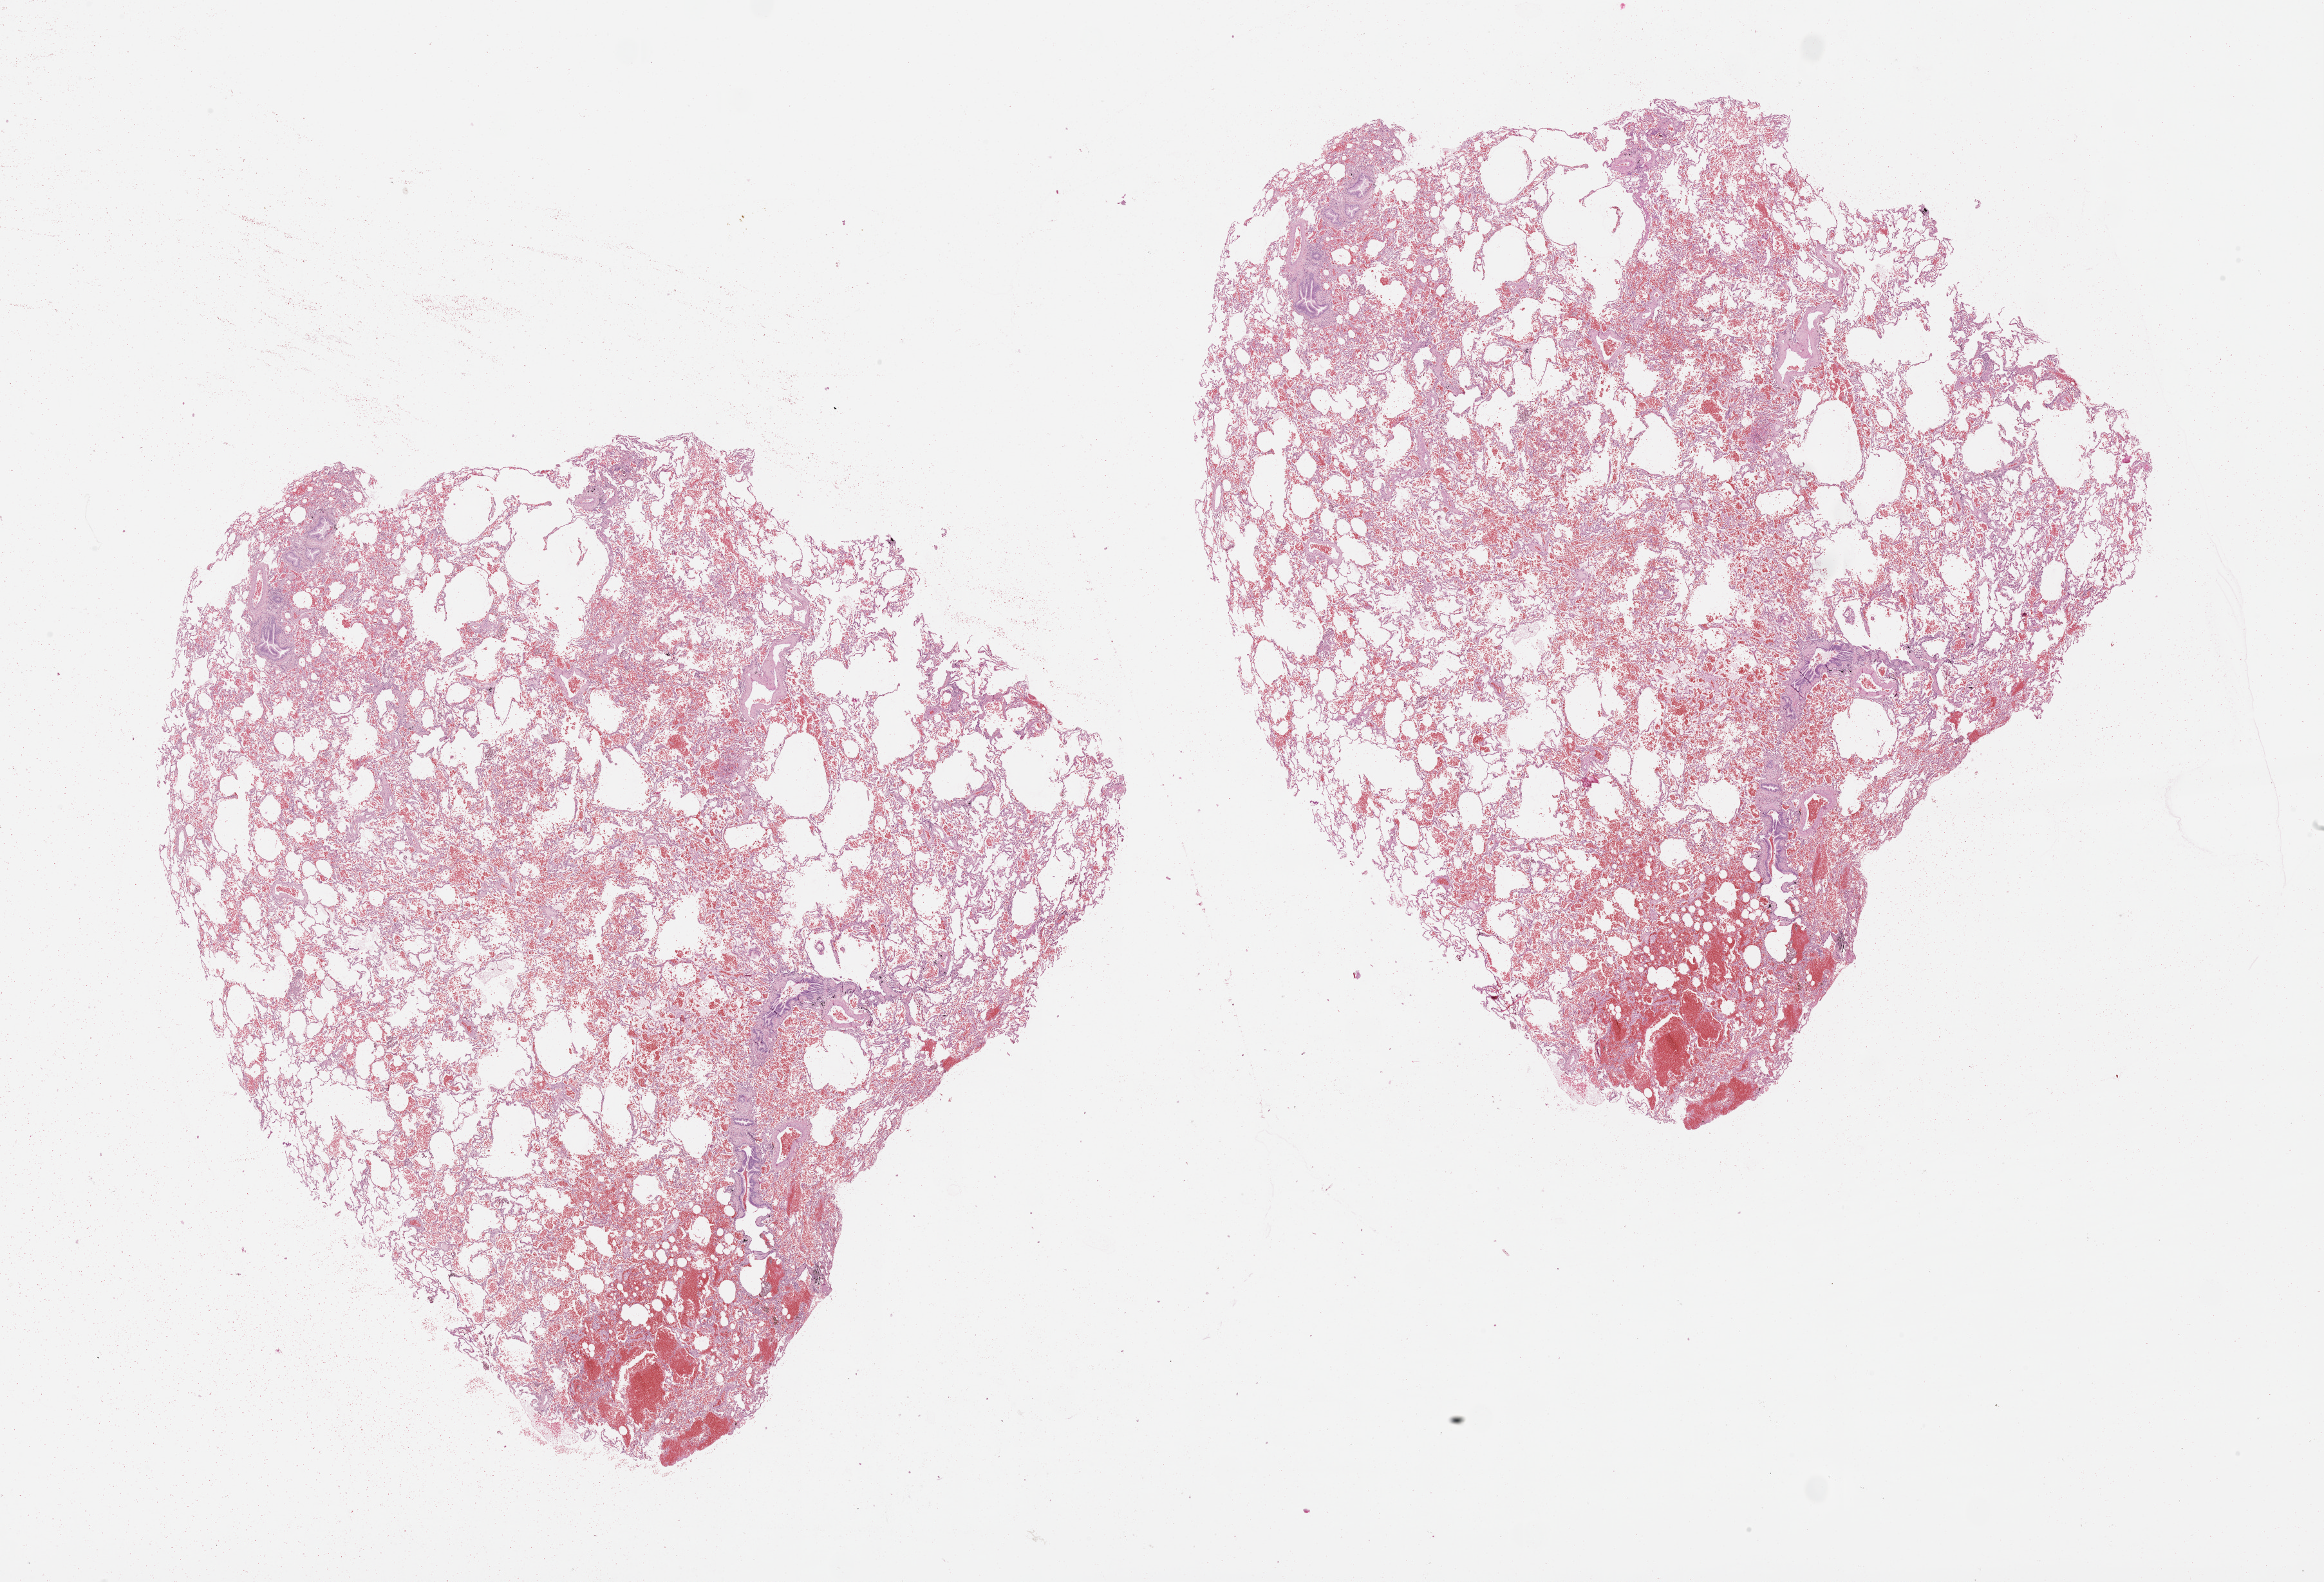
H&E whole-slide image — low-resolution overview of the scanned area, about 29.1 x 19.8 mm (acquisition: 20x scan), normal (non-tumour) tissue sample, lung. 69-year-old male patient.
This section: normal (non-tumour) tissue from the same patient. Patient diagnosis (cohort enrolment): squamous cell carcinoma (lung).